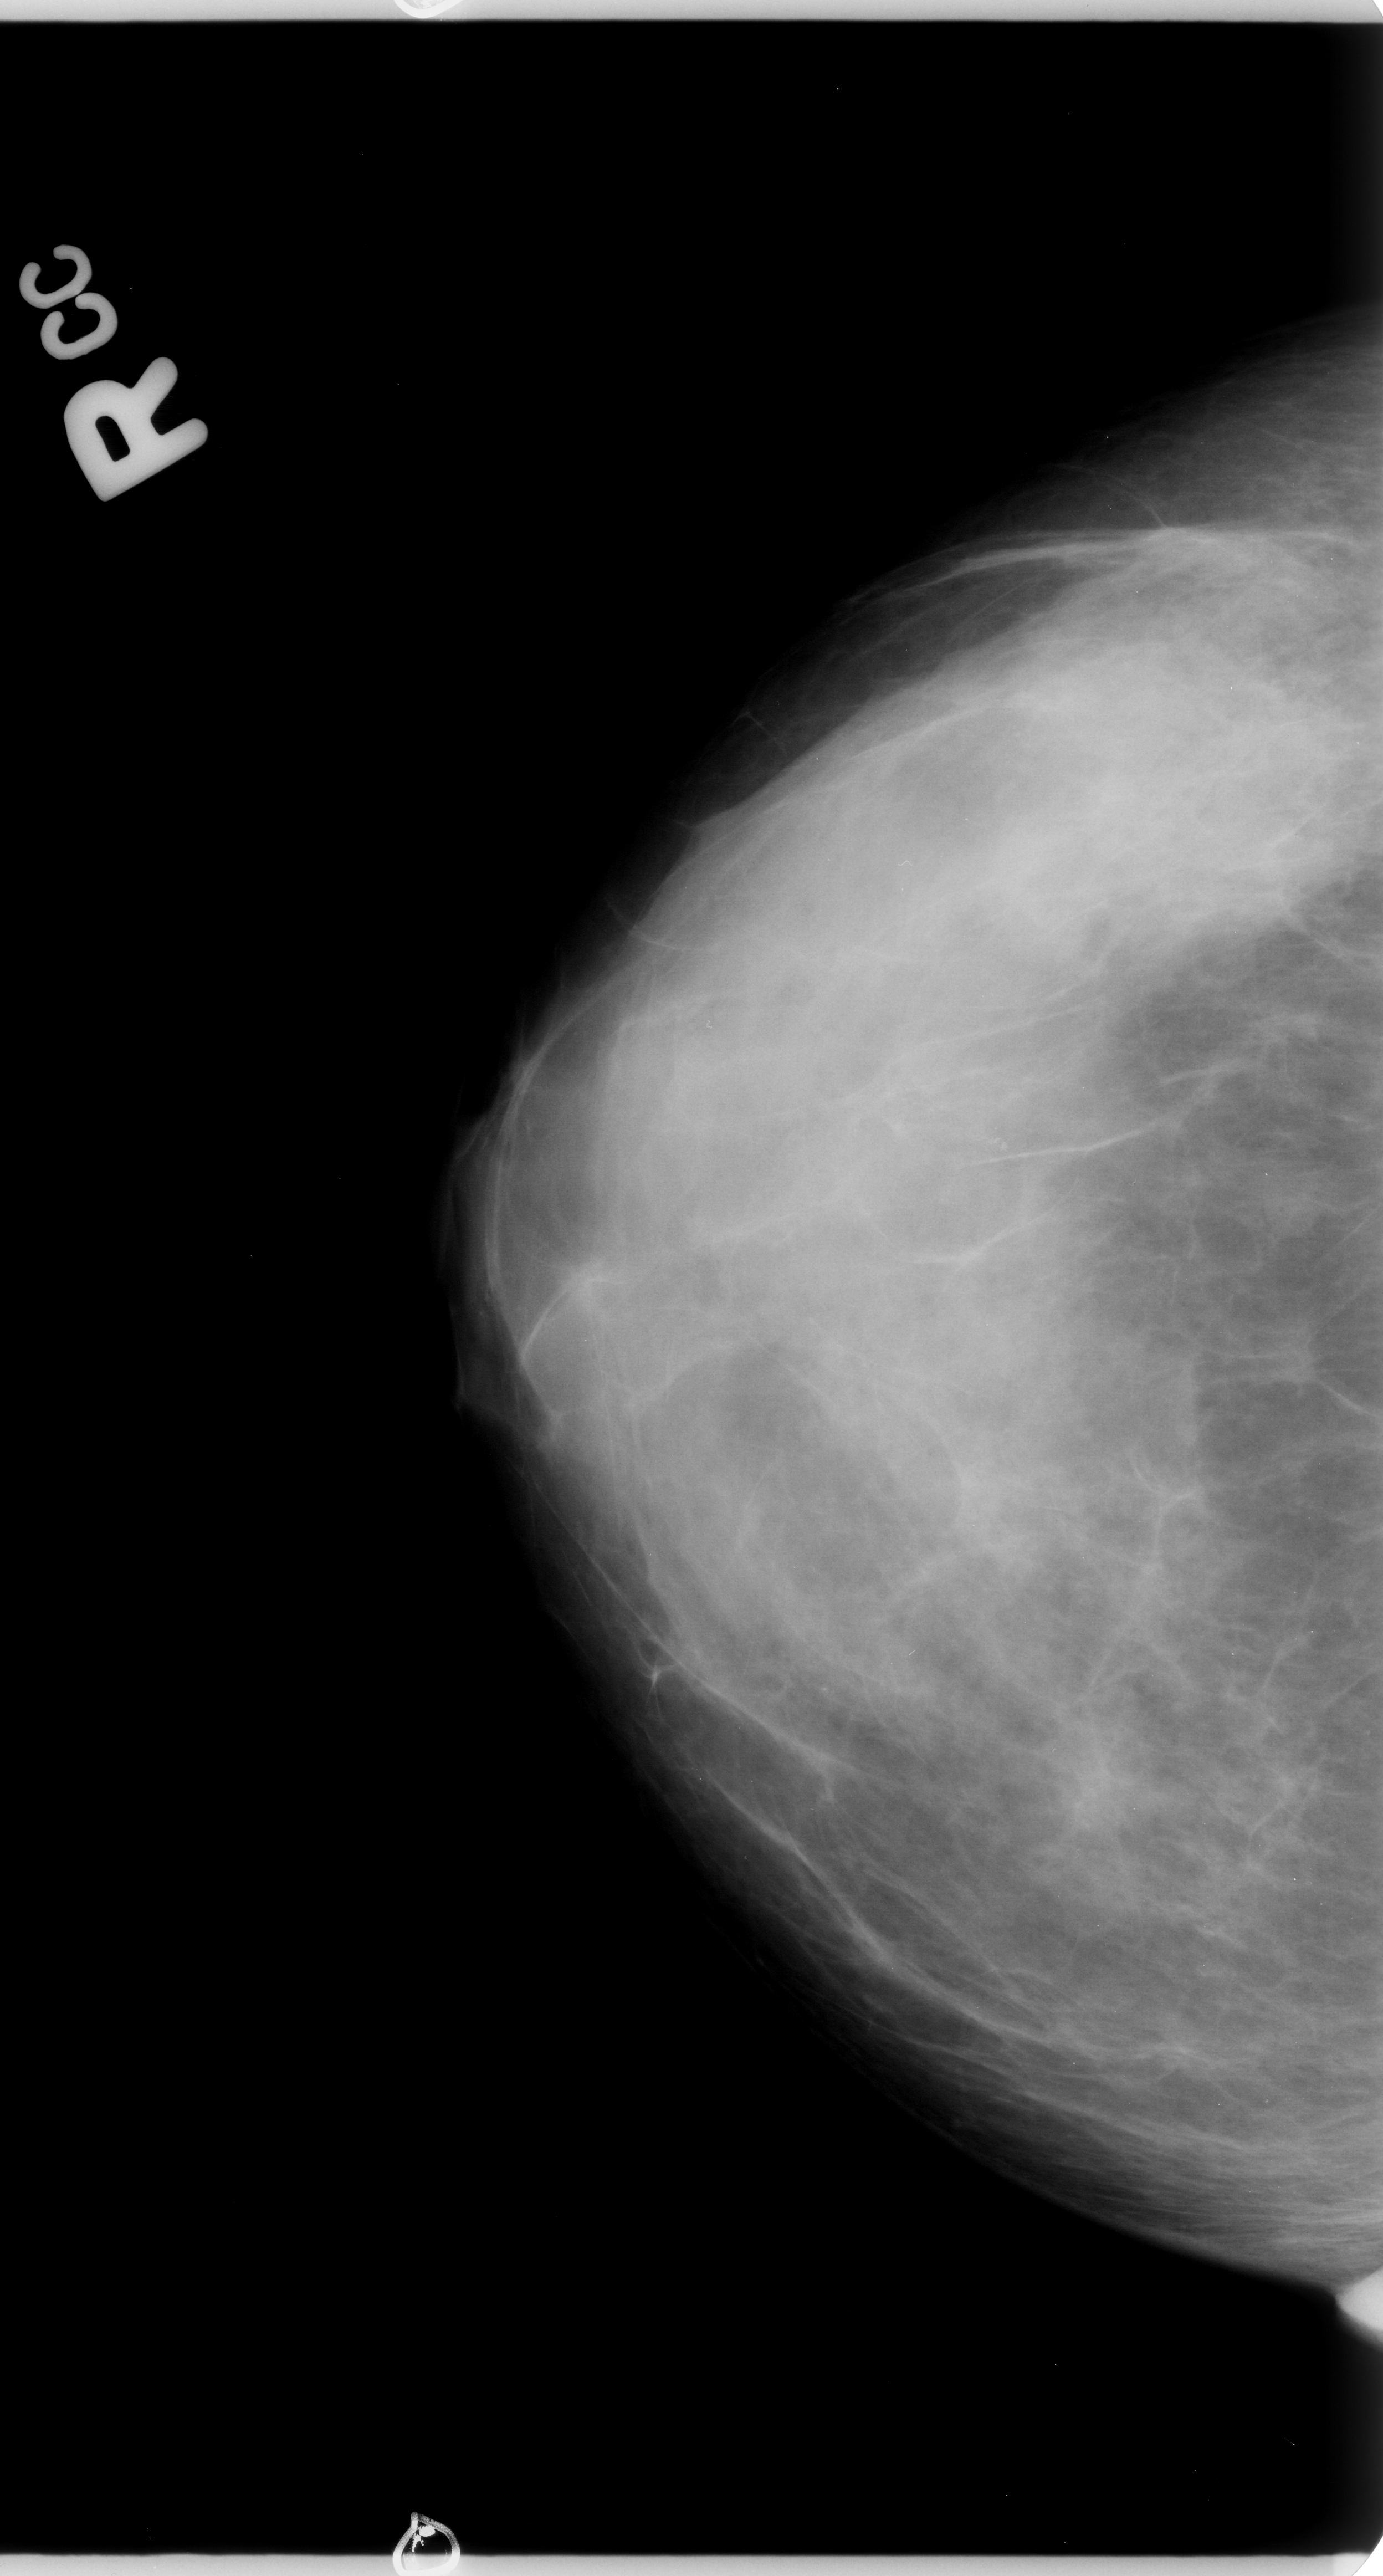
Mammogram (digitized film). Right breast. CC view. BI-RADS breast density category 4 (scale 1–4). 1383 × 2576 image matrix.
Expert-marked regions of interest on this image (one box per marked abnormality):
- calcifications, morphology pleomorphic, distribution clustered; BI-RADS assessment category 4; subtlety rating 3 on a 1 (subtle) to 5 (obvious) scale; pathology result (as recorded, not read from the image): benign: bounding box <926,1081,1065,1225> (left, top, right, bottom; pixels)